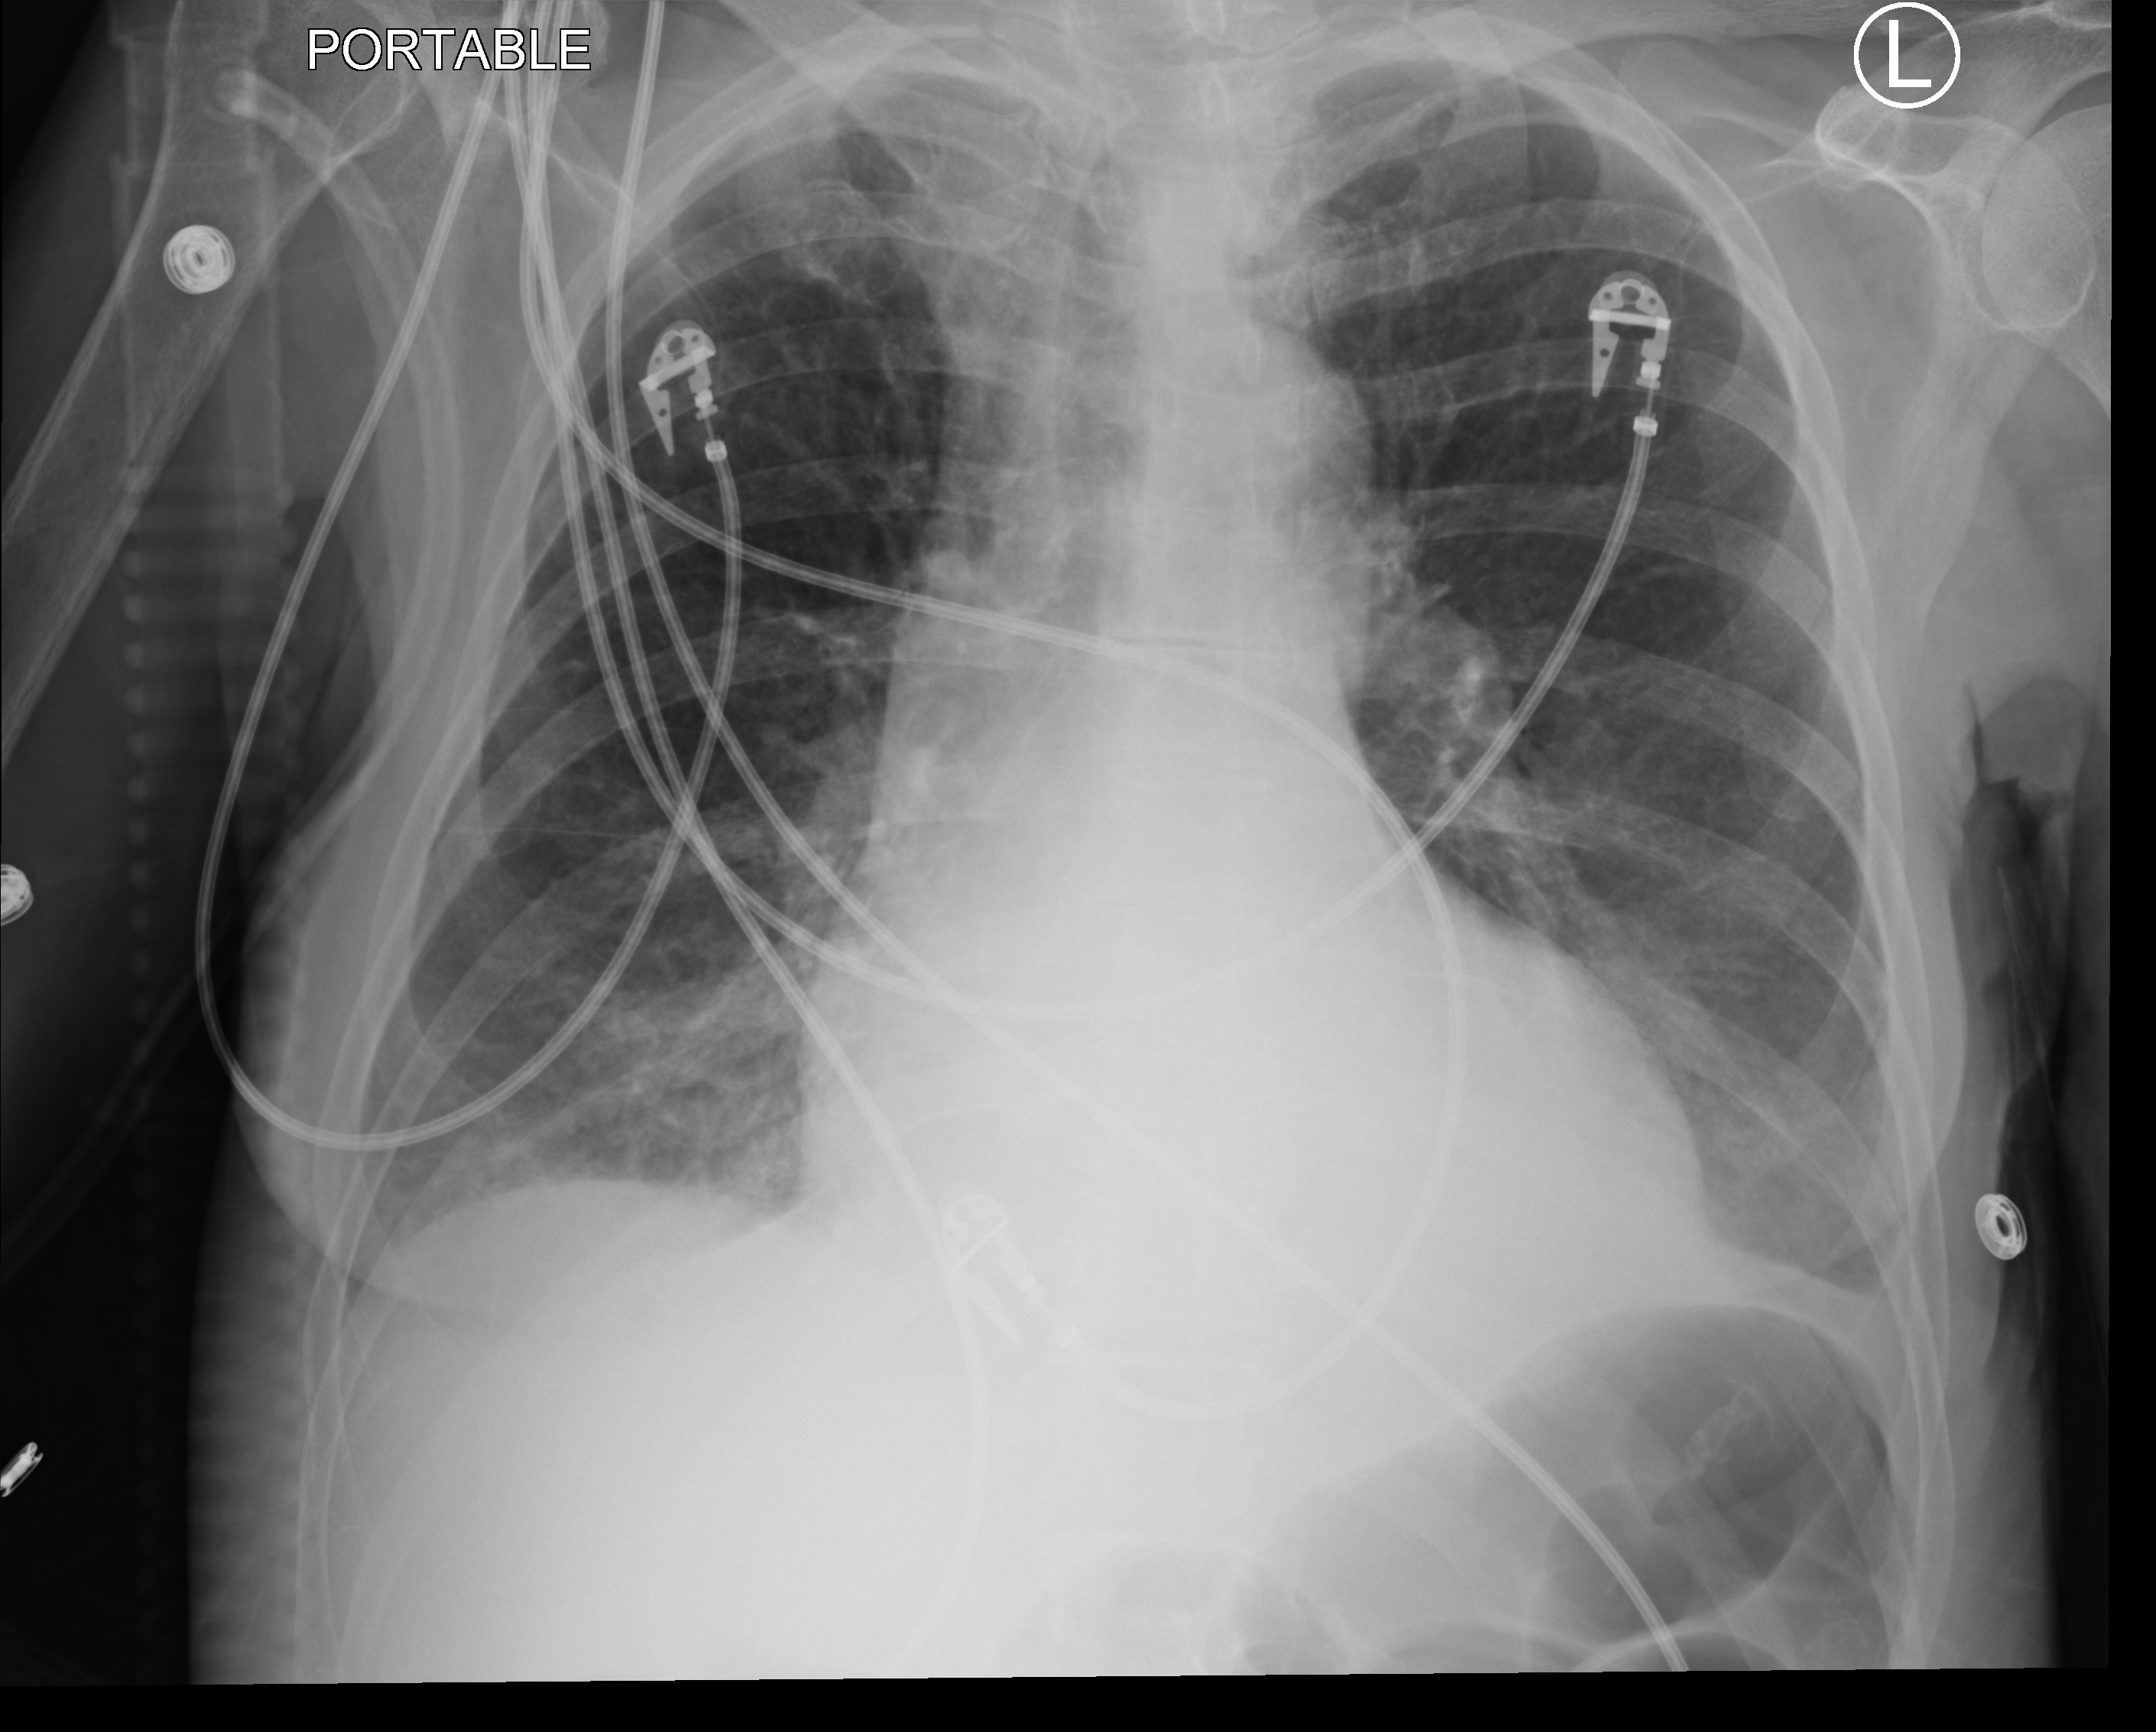
Chest X-ray (portable), anteroposterior (AP) projection. Patient hospitalised with COVID-19; female, aged 60–74 years.
From the hospital-stay record, not from the radiograph (when in the stay this image was taken is not recorded): mechanically ventilated during this hospital stay: yes; admitted to intensive care during this hospital stay: yes.